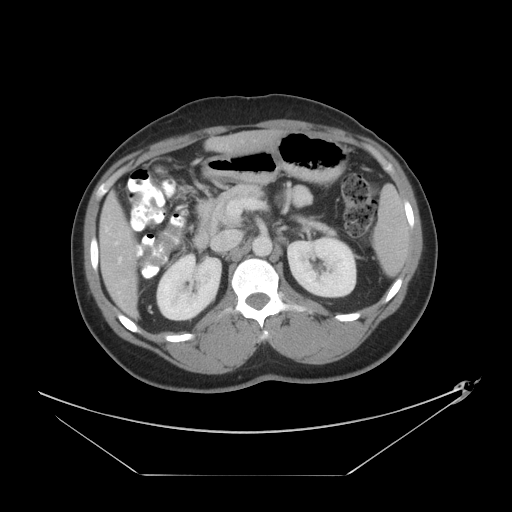
Contrast-enhanced abdominal CT, one axial slice; position 21 of 44 along the scan axis; 120 kVp; soft-tissue window (W 400 / L 40 HU); 512 × 512 image matrix, field of view 466 × 466 mm. Male patient, age 49 years. From the clinical record (not read from this slice): diagnosis: colorectal cancer liver metastases, imaged before liver resection; multiple liver metastases: no.
Outlined on this slice (expert manual segmentation):
- hepatic veins: bounding box [x1, y1, x2, y2] px = [118, 225, 143, 263]
- liver: [100, 131, 283, 317]
- planned liver remnant (the part of the liver to remain after resection): [217, 131, 283, 154]
- portal vein (with intrahepatic branches): [106, 228, 108, 231]